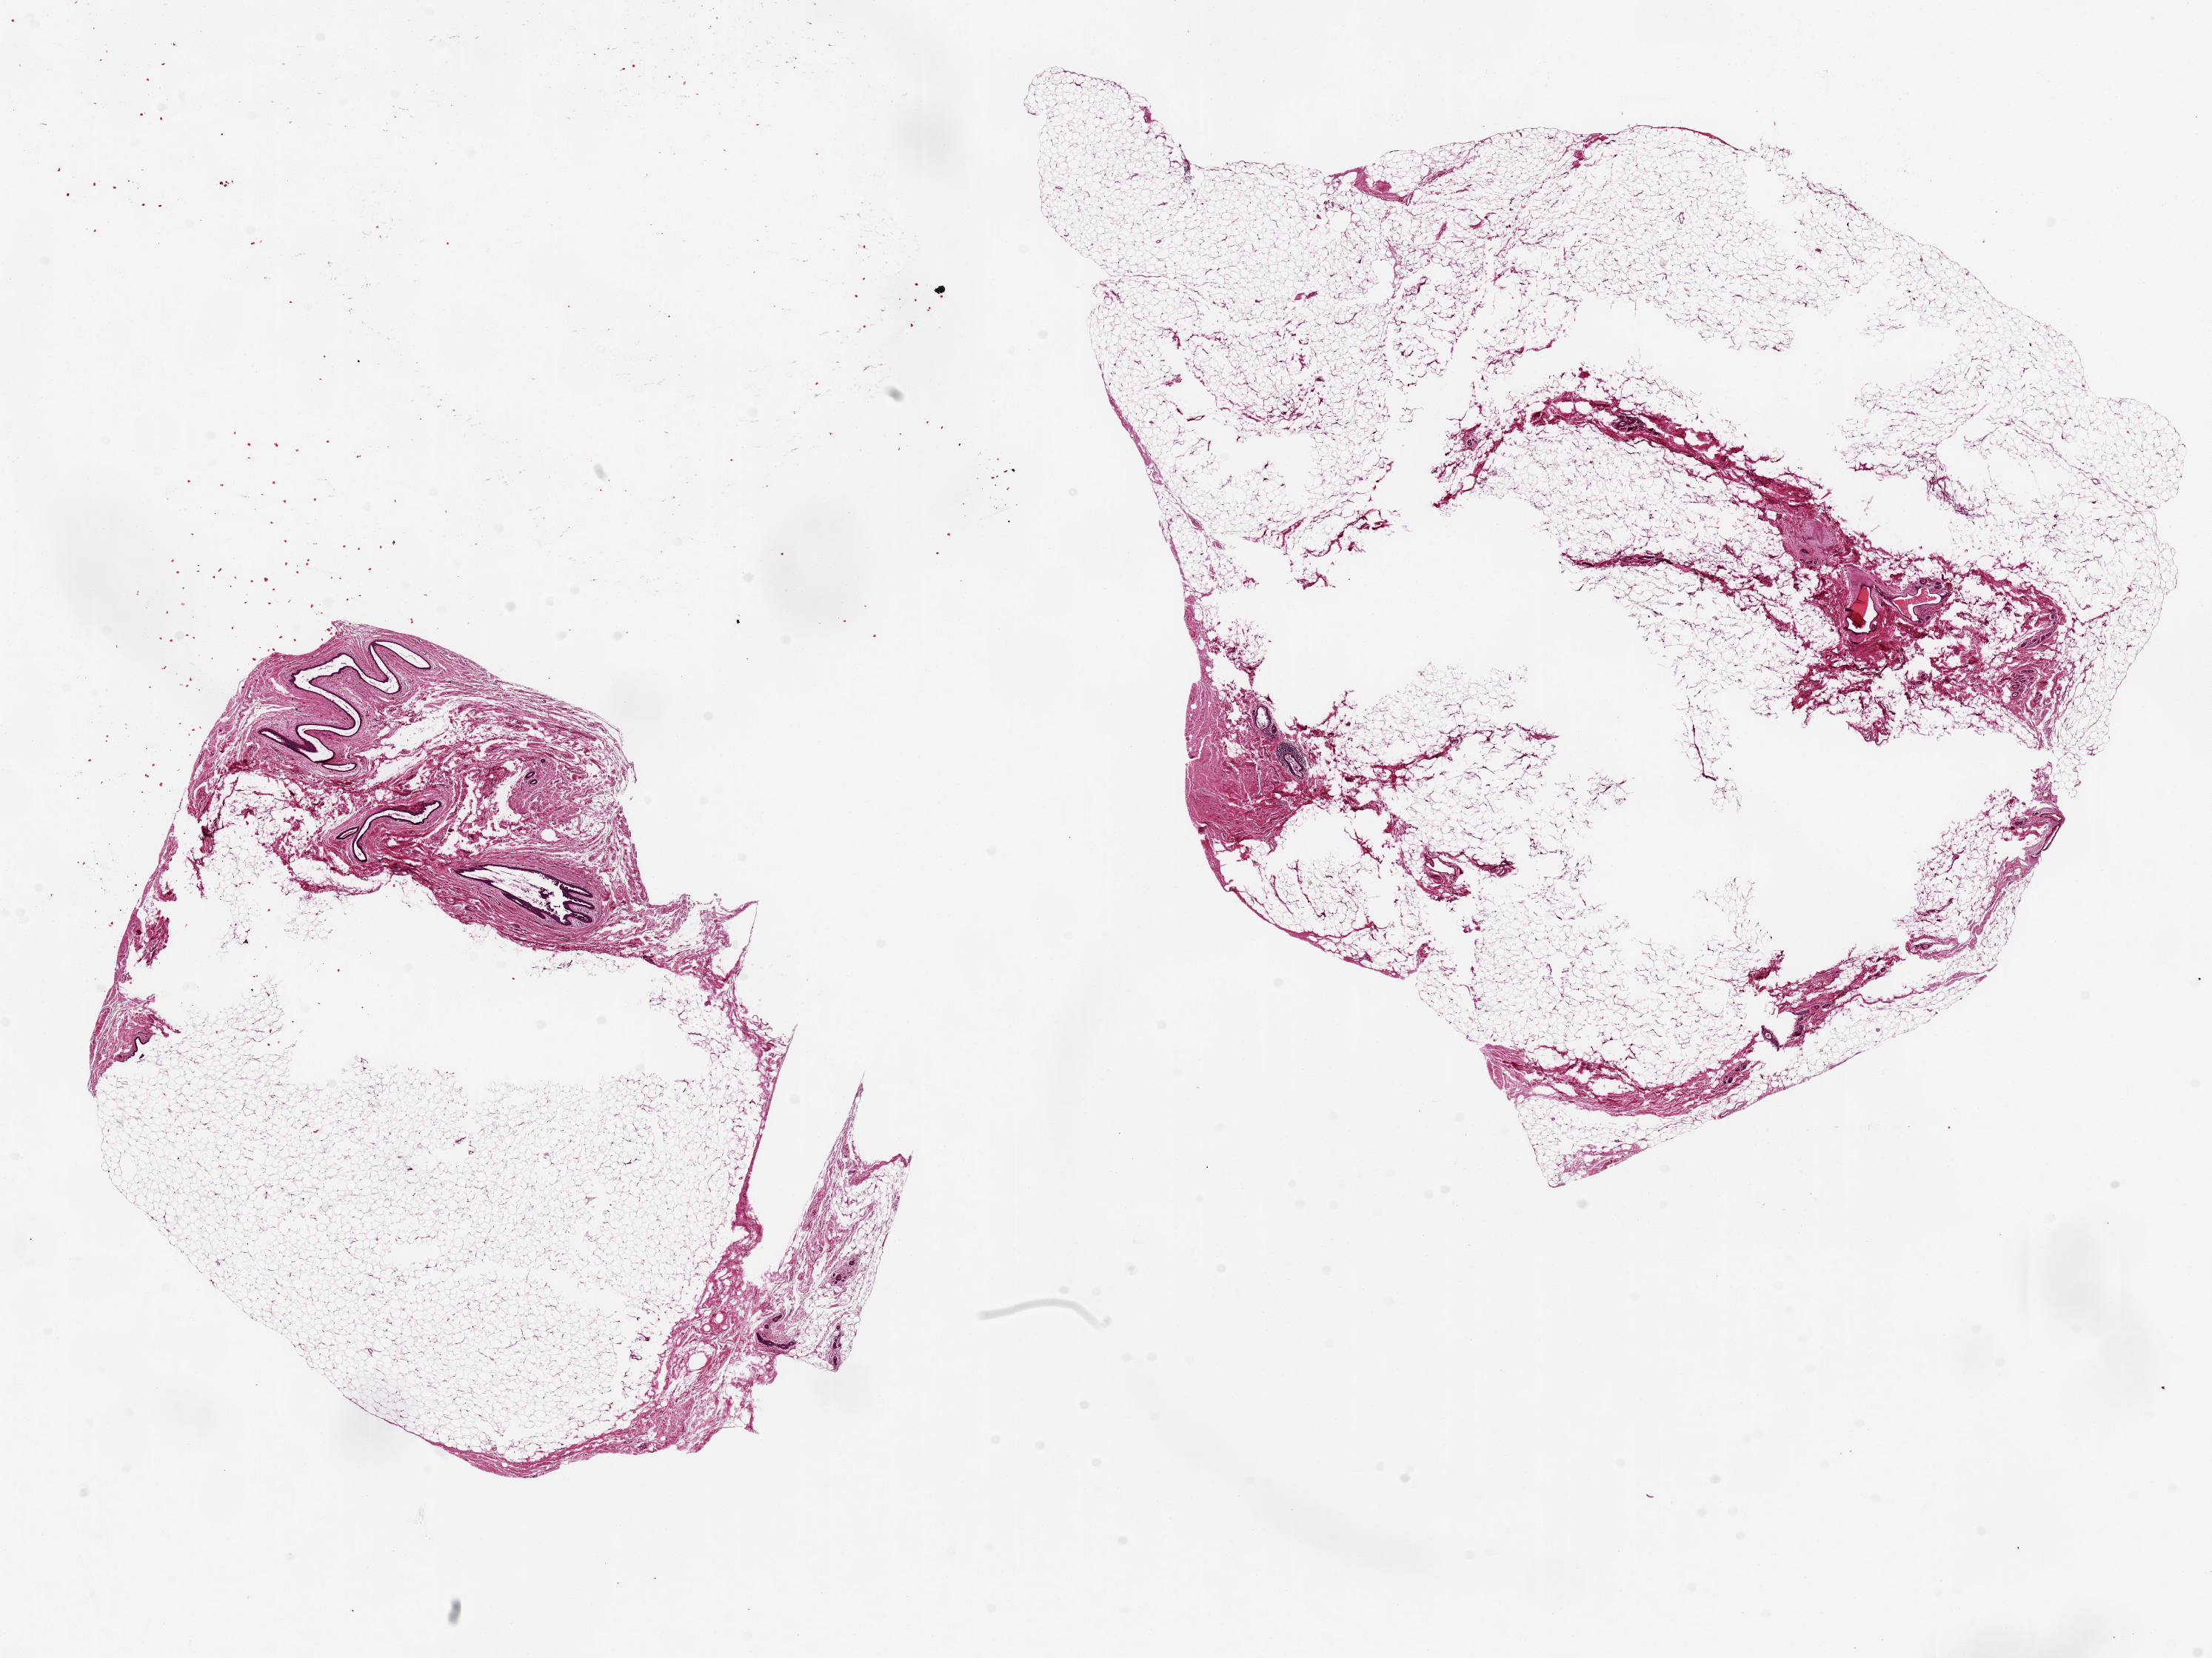
Digitized hematoxylin and eosin (H&E)-stained section — whole scanned area (about 23.6 x 17.7 mm, from a 20x scan) shown as a low-resolution overview, PAXgene-fixed paraffin-embedded (PFPE) section, sampled site (target tissue): breast, donor tissue sample.
Review note (as recorded): 2 pieces 9x8 & 13x10 mm; large ducts, no lobules; 80-90% adipose; central unfixed adipose especially in large piece.